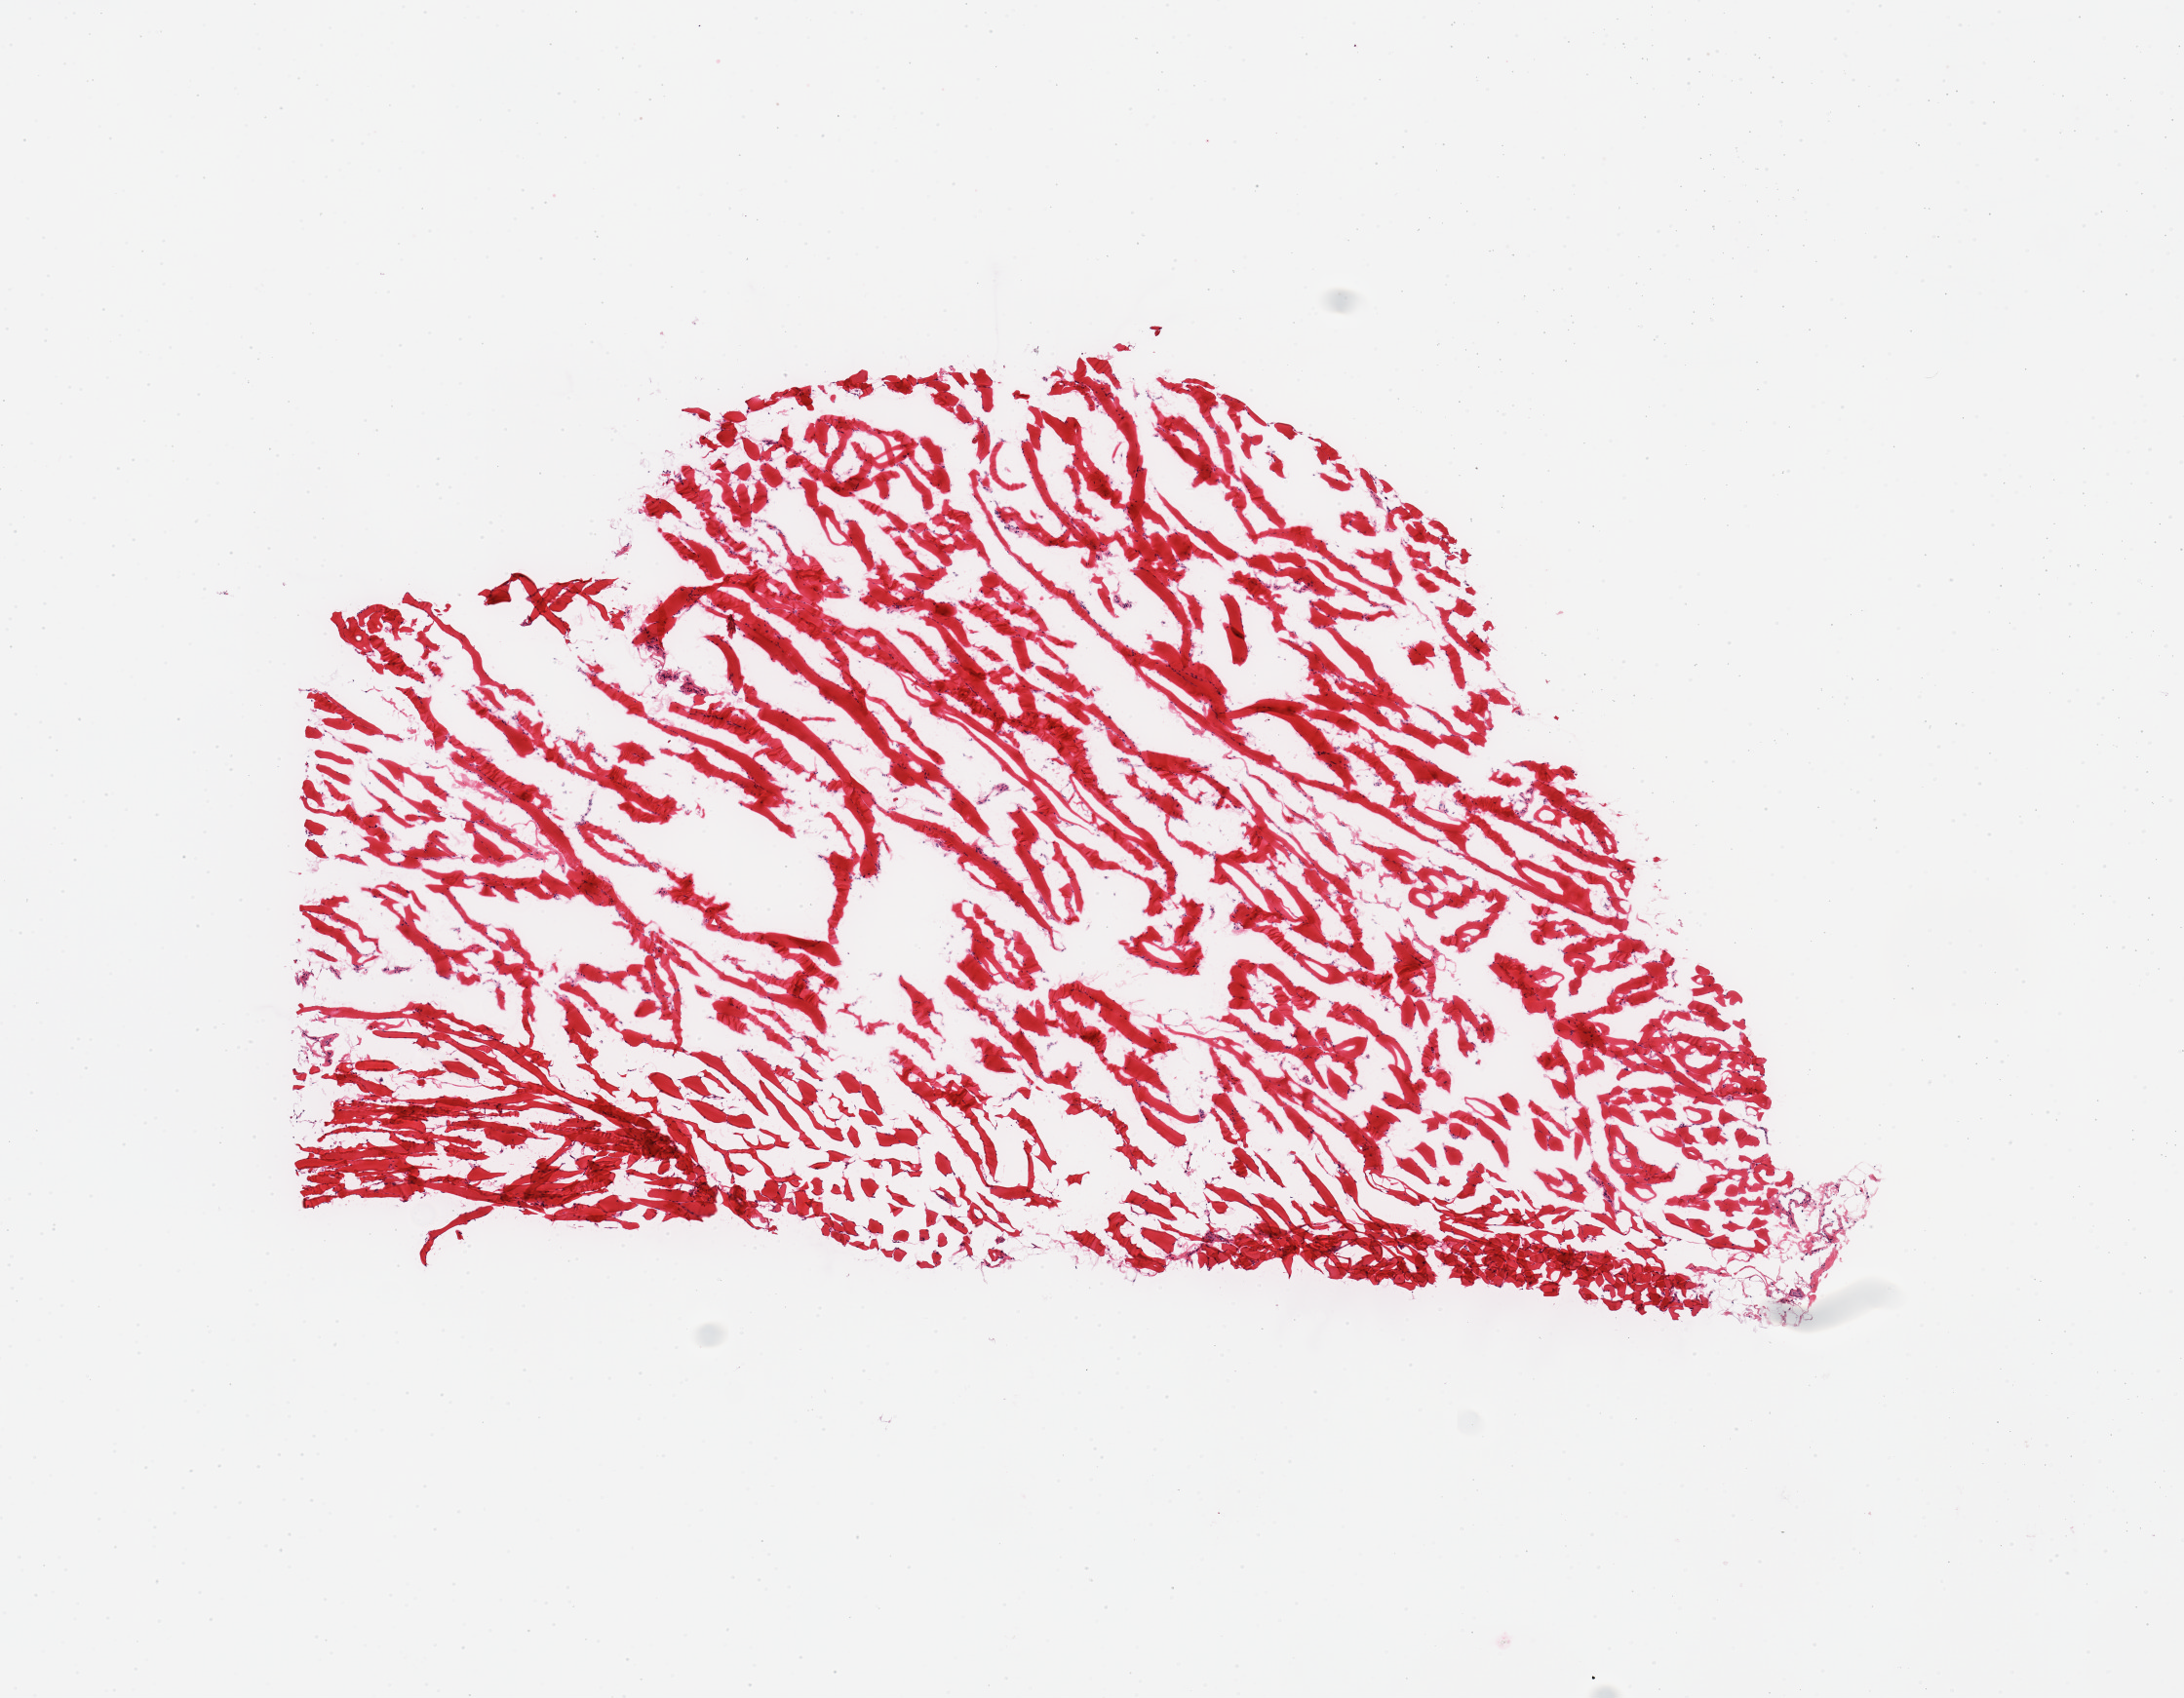
Hematoxylin and eosin (H&E) whole-slide image — a low-resolution overview of the entire scanned area, about 8.9 x 6.9 mm (from a 20x scan); frozen section; sampled site (target tissue): skeletal muscle; tissue donor sample. Donor: female.
- pathologist's review note for this sample: 1 piece; comparable to content in PAXgene sample